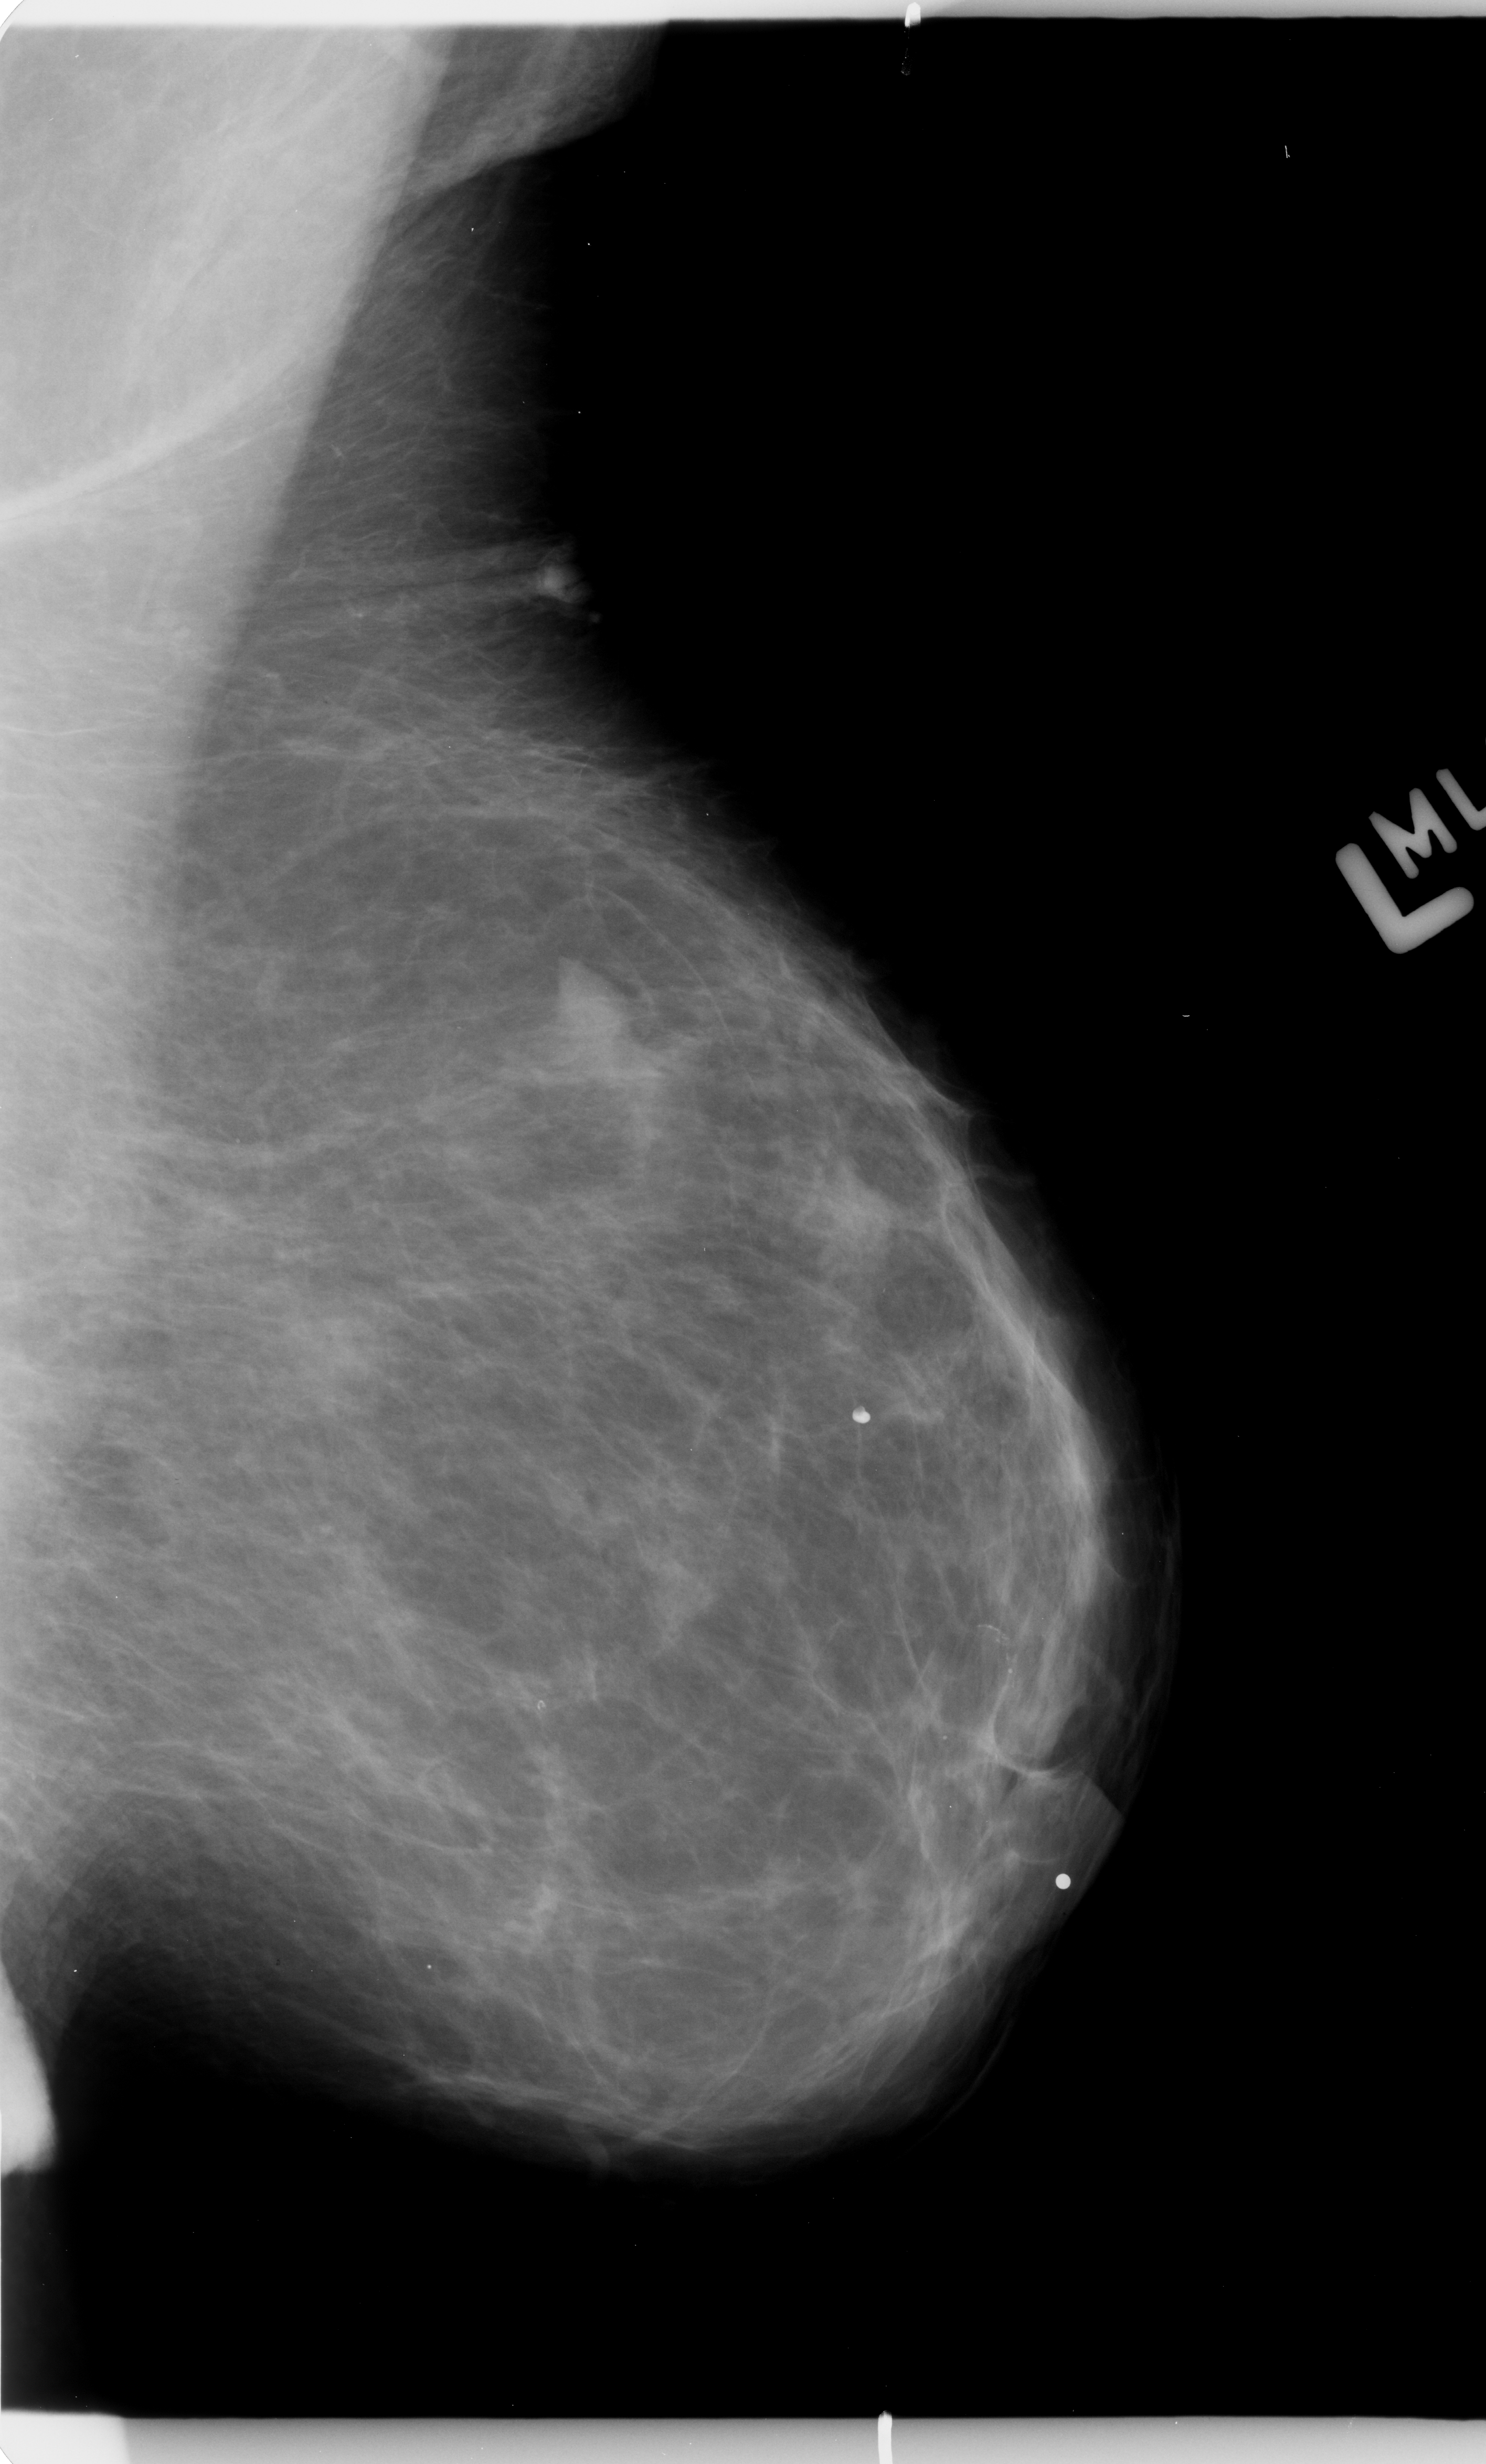
Digitized screen-film mammogram. Left breast. Mediolateral oblique (MLO) view. Breast composition: scattered fibroglandular densities (BI-RADS density category 2 of 4). 1486 × 2464 image matrix.
Expert-marked regions of interest on this image (one box per marked abnormality):
- mass, shape irregular, margins ill defined; BI-RADS assessment category 4; pathology result (as recorded, not read from the image): benign: bounding box (x1, y1, x2, y2) in pixels: (549, 986, 692, 1147)